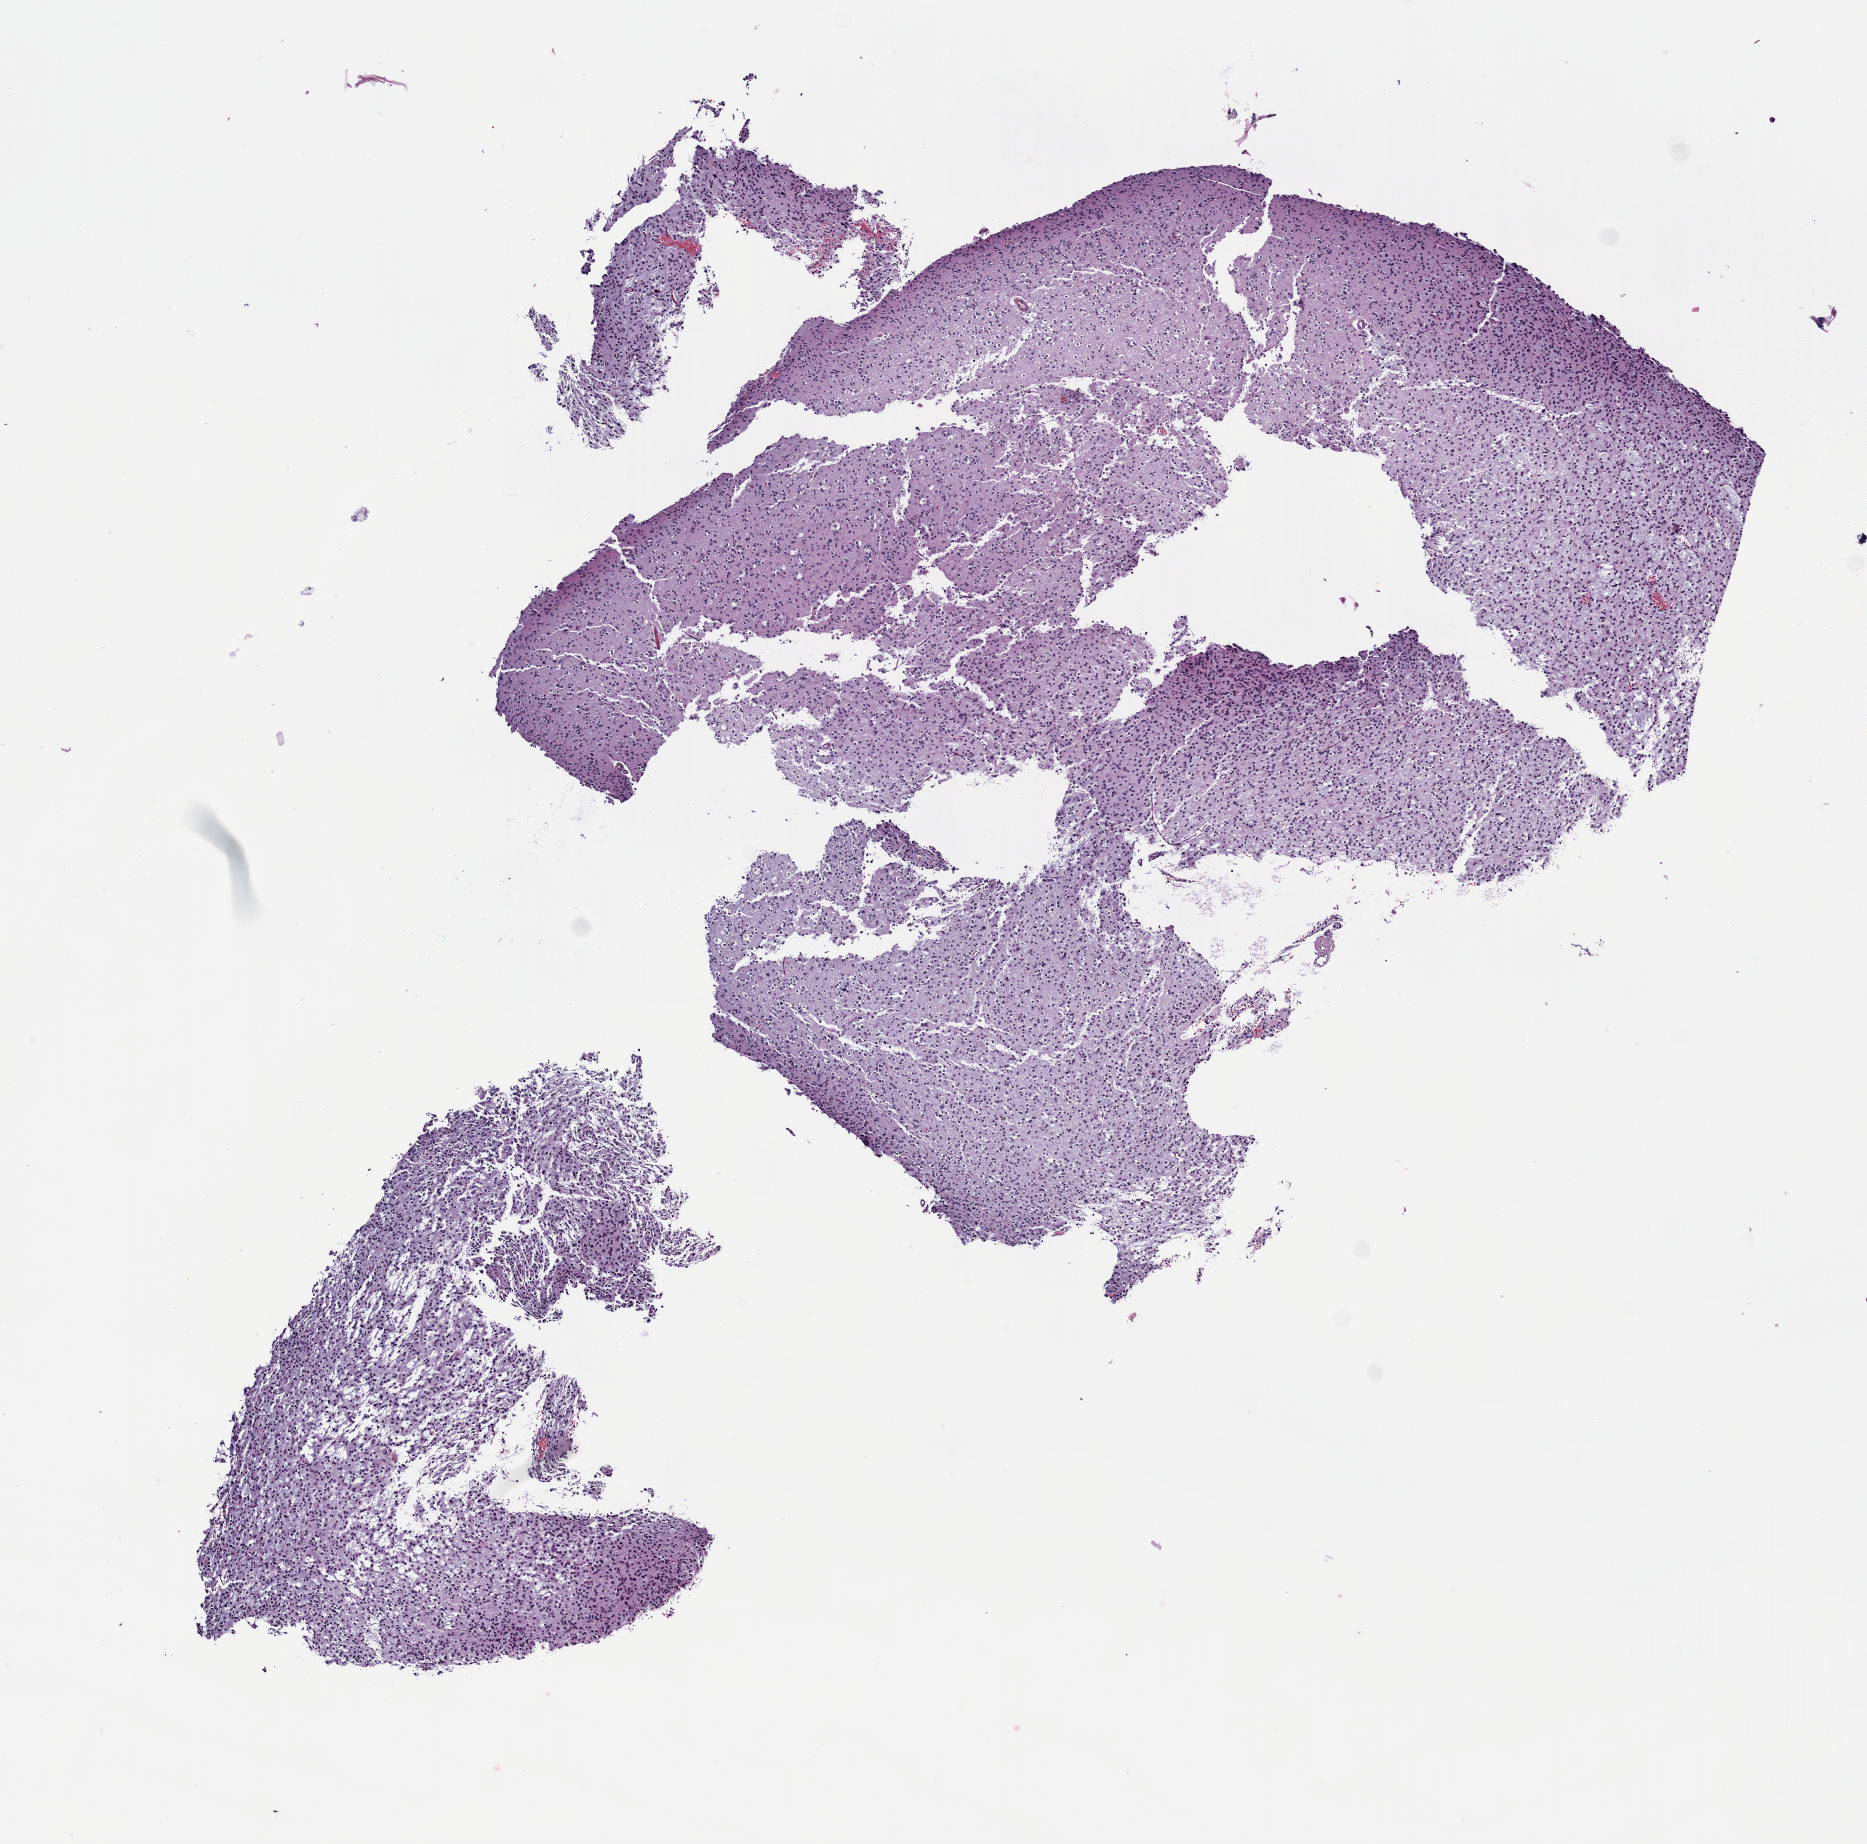
H&E whole-slide image — low-resolution overview of the scanned area, about 7.6 x 7.5 mm (from a 40x scan). Formalin-fixed paraffin-embedded (FFPE) diagnostic section. Brain, primary tumour sample. Patient: female, age at initial diagnosis 50 years. Histologic grade: G2 (moderately differentiated).
Histologic diagnosis: Oligodendroglioma, NOS (cerebrum). Laterality: right.